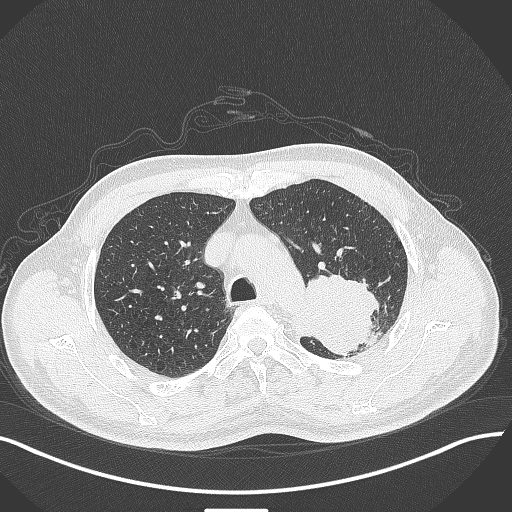
Chest CT, one axial slice; slice 317 of 429 in the series (ordered by position); reconstruction kernel B70f; 120 kVp; lung window (W 1500 / L -600 HU); 1 mm slice thickness; 512 × 512 image matrix, field of view 400 × 400 mm. Patient: male, 55 years. From the clinical record (not read from this slice): clinical TNM (as recorded): T3 N0 M1c; histopathological grade: G3.
Structures marked on this image (rectangle marked by the reading radiologist):
- lung tumour (recorded histology: adenocarcinoma): box from (x=291, y=269) to (x=383, y=361) px